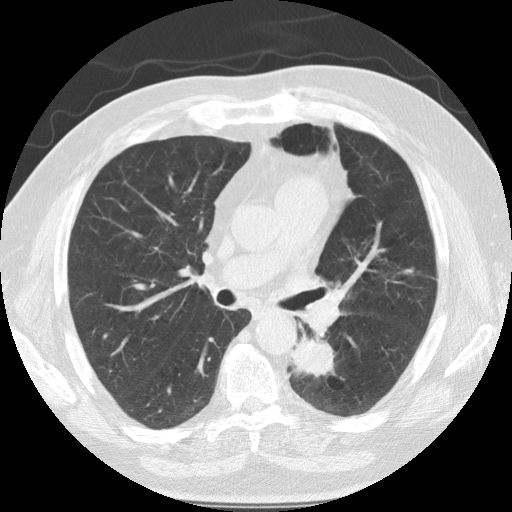
Low-dose screening chest CT, axial slice, baseline annual screen, lung window (W 1500 / L -600 HU), 2.5 mm slice thickness, slice 56 of 124 in the series. Male, age 68 years at enrolment.
Expert reader's lesion annotation, box from (x=279, y=317) to (x=352, y=396) px. The screening reader recorded 3 non-calcified nodules or masses ≥4 mm on this exam; which of them this box marks is not recorded. Official screen result: positive, change unspecified: nodule(s) >= 4 mm or enlarging nodule(s), mass(es), or other non-specific abnormalities suspicious for lung cancer. Lung cancer was diagnosed 35 days after this screen: squamous cell carcinoma, NOS, left lower lobe, poorly differentiated (G3), stage IIB (AJCC 6th edition), 40 mm at pathology.